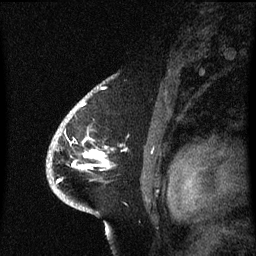
Breast MRI (dynamic contrast-enhanced), one sagittal slice. Slice 46 of 60 in the series (ordered by position). Dynamic contrast-enhanced series, image 2 of 3 at this slice position (ordered by acquisition). 1.5 T. TE 4.2 ms, TR 8.4 ms. 2.1 mm slice thickness. 256 × 256 image matrix, field of view 200 × 200 mm. Female patient, age 53 years. From the clinical record (not read from this slice): setting: breast cancer imaged before/during neoadjuvant chemotherapy; receptor status: HR-positive, HER2-negative.
Outlined on this slice (semi-automatic segmentation, software-assisted and operator-edited):
- analysis volume of interest (the breast-tissue region the enhancement analysis was run in; not a lesion): bounding box (x1, y1, x2, y2) in pixels: (49, 108, 108, 201)
- tumour enhancement mask (voxels above the 70 % enhancement threshold inside the analysis volume of interest): (59, 152, 107, 183)